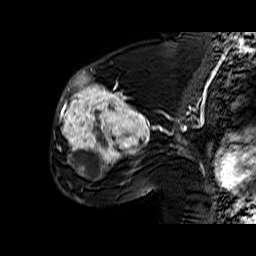
Breast MRI (dynamic contrast-enhanced), one sagittal slice; position 34 of 60 along the scan axis; dynamic contrast-enhanced series, time point 2 of 6 at this slice position (early post-contrast); 1.5 T; TE 6.4 ms, TR 32.9 ms; 256 × 256 image matrix. Female patient. Case-level facts recorded for this patient, not image findings: setting: breast cancer imaged before/during neoadjuvant chemotherapy; receptor status: triple-negative.
Outlined on this slice (semi-automatic segmentation, software-assisted and operator-edited):
- analysis volume of interest (the breast-tissue region the enhancement analysis was run in; not a lesion): box from (x=57, y=65) to (x=159, y=174) px
- tumour enhancement mask (voxels above the 100 % enhancement threshold inside the analysis volume of interest): (x=58, y=71)–(x=150, y=174)